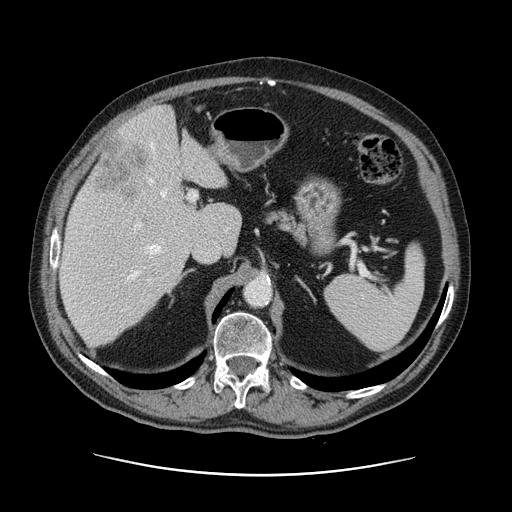
Contrast-enhanced abdominal CT, one axial slice; slice 82 of 141 in the series (ordered by position); intravenous contrast given; soft-tissue window (W 400 / L 40 HU); 512 × 512 image matrix, field of view 395 × 395 mm. Male patient, age 72 years. From the clinical record (not read from this slice): diagnosis: colorectal cancer liver metastases, imaged before liver resection; multiple liver metastases: yes; largest metastasis: 5.4 cm; chemotherapy before resection: yes.
Annotated regions visible in this slice (expert manual segmentation):
- hepatic veins: bounding box <128,143,167,280> (left, top, right, bottom; pixels)
- liver: <59,106,242,346>
- planned liver remnant (the part of the liver to remain after resection): <59,132,242,346>
- portal vein (with intrahepatic branches): <92,191,198,281>
- liver metastasis: <95,141,150,200>